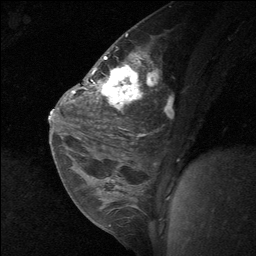
Breast MRI (dynamic contrast-enhanced), one sagittal slice; slice 38 of 64 in the series (ordered by position); dynamic contrast-enhanced study with each time point stored as its own series, time point 2 of 3 at this slice position (early post-contrast, ordered by acquisition time); 1.5 T; TE 4.8 ms, TR 27 ms; 2 mm slice thickness; 256 × 256 image matrix. Patient: female, 26 years. Case-level facts recorded for this patient, not image findings: setting: breast cancer imaged before/during neoadjuvant chemotherapy; receptor status: HR-positive, HER2-negative.
Annotated regions visible in this slice (semi-automatic segmentation, software-assisted and operator-edited):
- analysis volume of interest (the breast-tissue region the enhancement analysis was run in; not a lesion): bounding box [x1, y1, x2, y2] px = [86, 43, 148, 138]
- tumour enhancement mask (voxels above the 90 % enhancement threshold inside the analysis volume of interest): [92, 55, 139, 108]